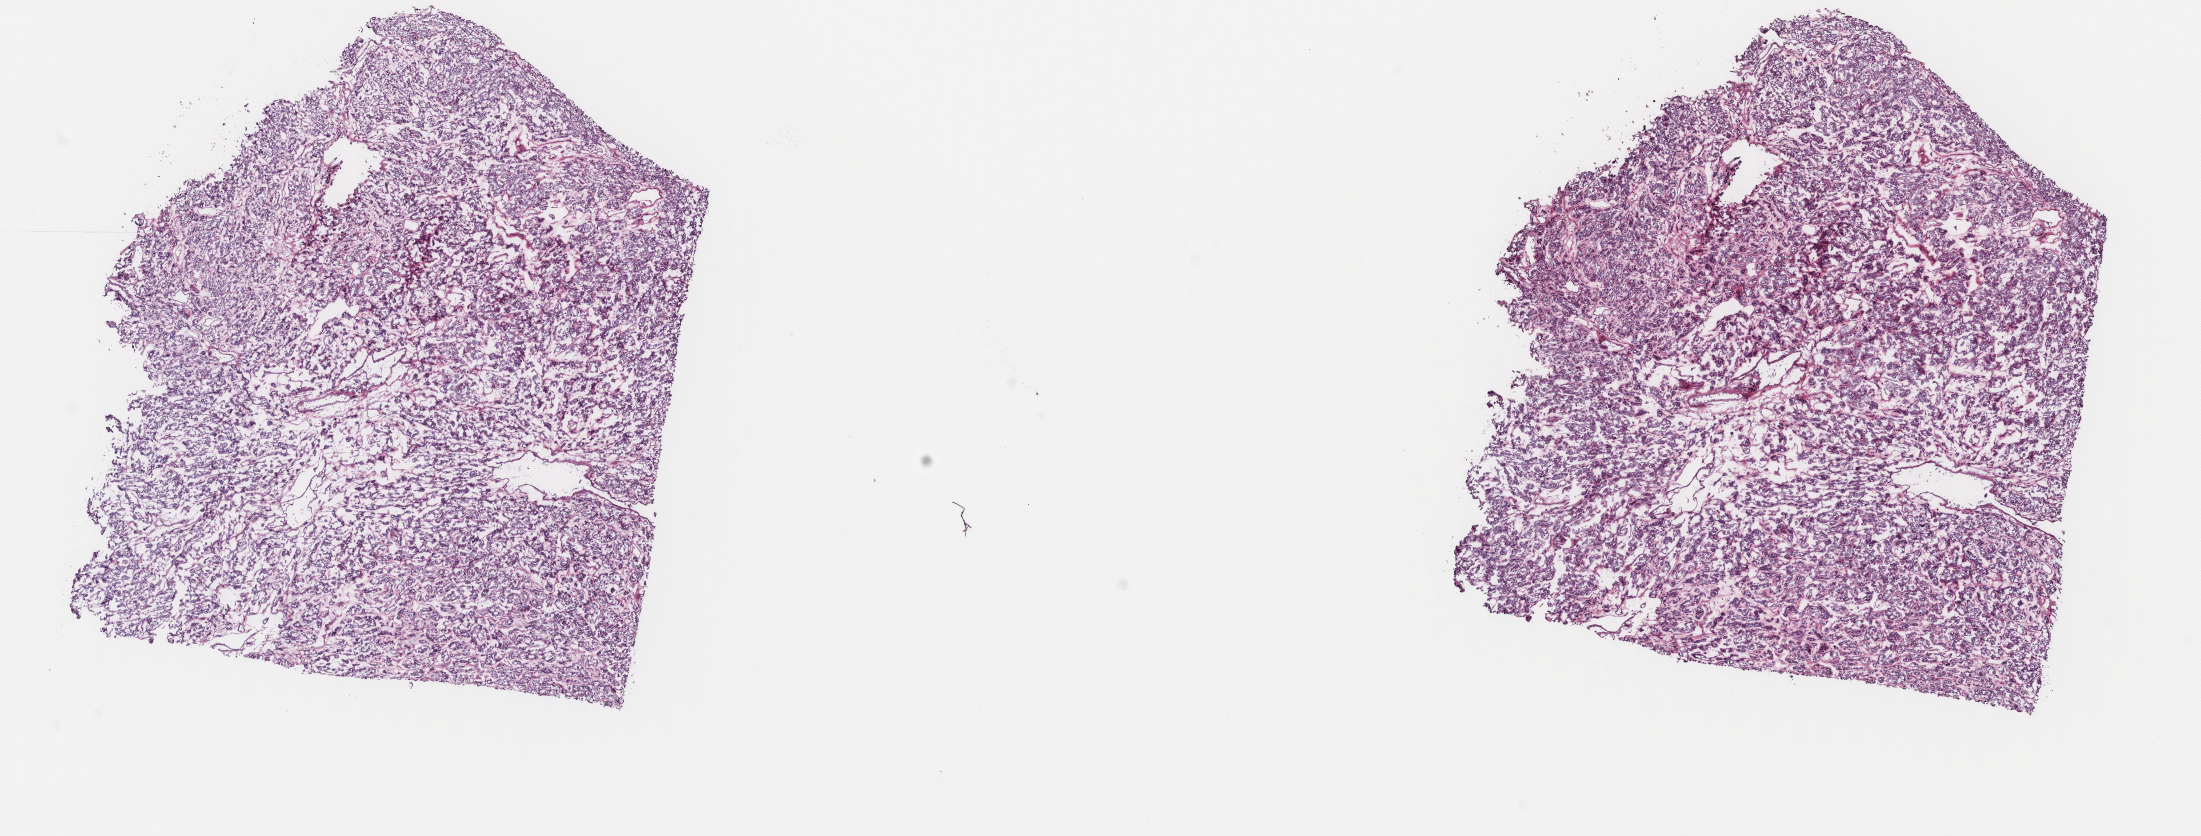
Whole-slide histology image, H&E, shown as a low-resolution overview of the whole scanned area (about 17.5 x 6.6 mm, from a 40x scan); frozen section from the top of the tissue portion; thyroid, primary tumour sample. Female patient; age at initial diagnosis 56 years. Pathologist review of this section (percent, as recorded): tumour cells 100%, tumour nuclei 92%, normal cells 0%, stromal cells 0%, necrosis 0%. Inflammatory infiltration, as recorded: lymphocyte infiltration 0%, monocyte infiltration 0%, neutrophil infiltration 0%.
AJCC pathologic stage: I (7th edition). Lymph nodes positive (case pathology): 0 of 9 examined. Laterality: right. Diagnosis: Papillary adenocarcinoma, NOS (thyroid gland).